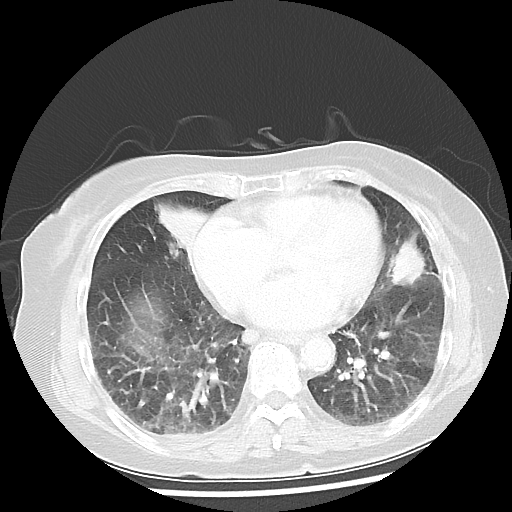
Chest CT, one axial slice; slice 17 of 50 in the series (ordered by position); 100 kVp; lung window (W 1500 / L -600 HU); 5 mm slice thickness; 512 × 512 image matrix, field of view 332 × 332 mm. Female patient, age 77 years. From the clinical record (not read from this slice): clinical TNM (as recorded): T2 N3 M1a.
Annotated regions visible in this slice (rectangle marked by the reading radiologist):
- lung tumour (recorded histology: adenocarcinoma): bounding box (x1, y1, x2, y2) in pixels: (389, 231, 428, 293)